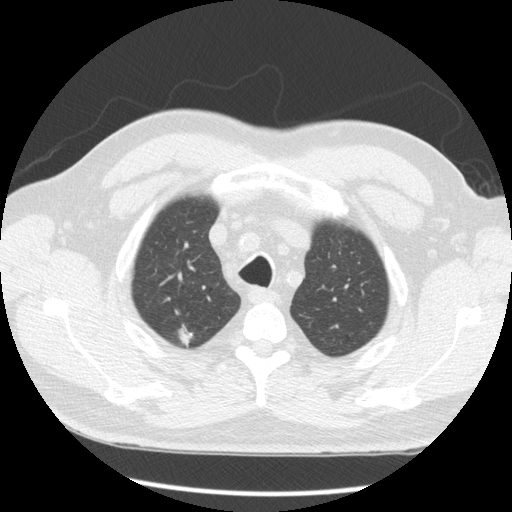
Low-dose screening chest CT, one axial slice. Slice 143 of 163 in the series (ordered by position). Reconstruction kernel STANDARD. Lung window (W 1500 / L -600 HU). 2.5 mm slice thickness. 512 × 512 image matrix, field of view 360 × 360 mm.
Structures marked on this image (manually delineated by an expert):
- lesion 1 (tumor, upper lobe of right lung): bounding box (x1, y1, x2, y2) in pixels: (178, 325, 193, 346)